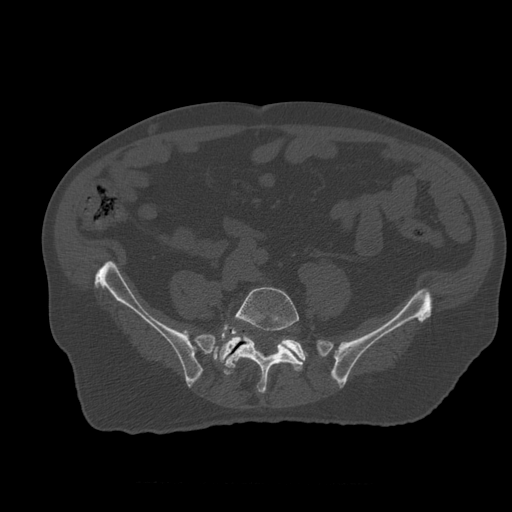
CT including the spine, one axial slice. Position 138 of 399 along the scan axis. 120 kVp. Bone window (W 1800 / L 400 HU). 1.25 mm slice thickness. 512 × 512 image matrix, field of view 407 × 407 mm. Patient age 73 years. Case-level facts recorded for this patient, not image findings: primary cancer: prostate; vertebrae with lytic lesions (as recorded): L2.
Structures marked on this image (semi-automatic segmentation, software-assisted and operator-edited):
- L5 vertebra: box from (x=213, y=287) to (x=303, y=394) px